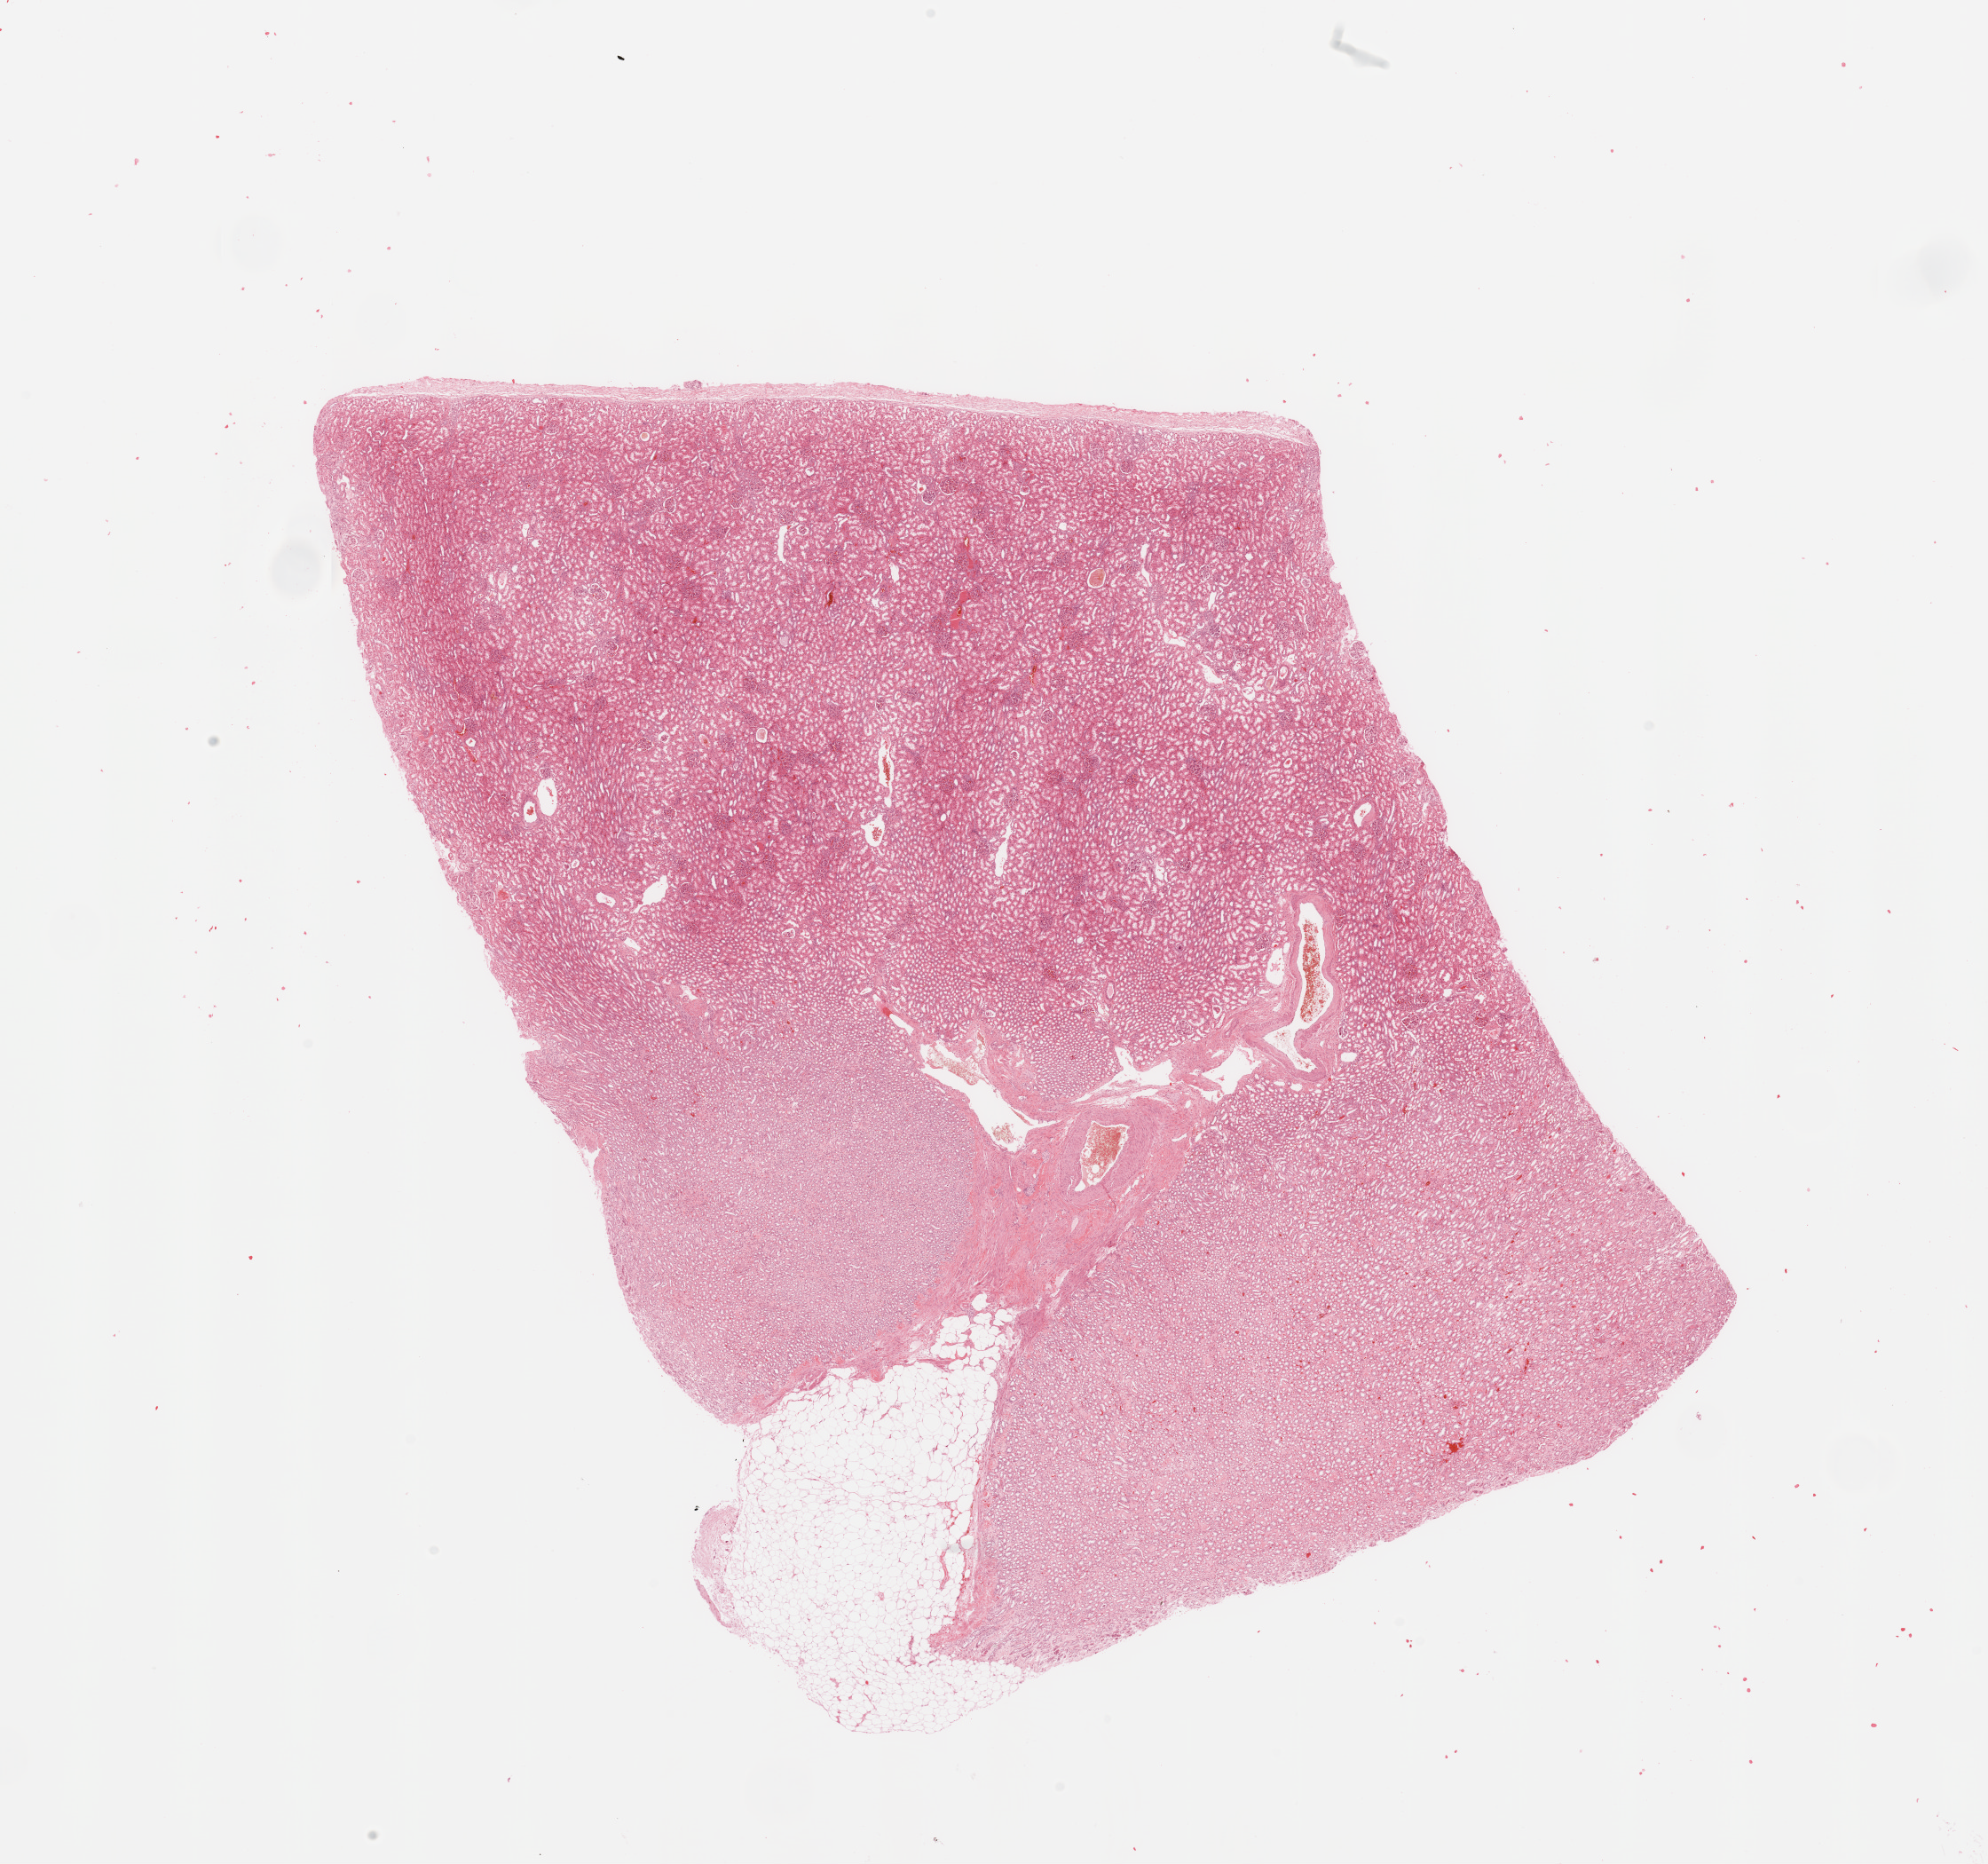
Hematoxylin and eosin (H&E) stained whole-slide image, whole scanned area (about 17.7 x 16.6 mm, from a 20x scan) shown as a low-resolution overview, normal (non-tumour) tissue sample, sampled site: kidney. 52-year-old male patient.
- this section: normal (non-tumour) tissue from the same patient
- patient diagnosis: Renal cell carcinoma, NOS